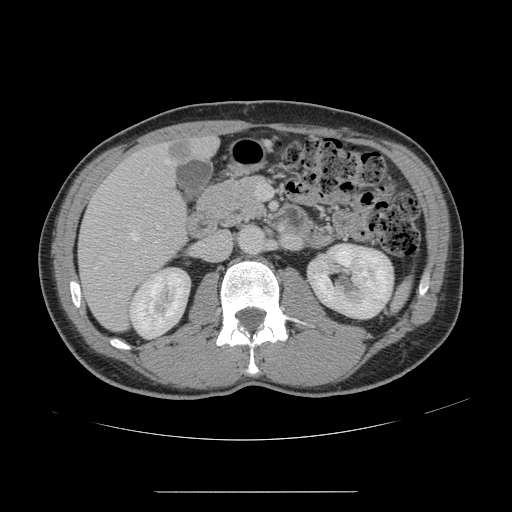
Contrast-enhanced abdominal CT, one axial slice. Slice 67 of 178 in the series (ordered by position). 120 kVp. Intravenous contrast given. Soft-tissue window (W 400 / L 40 HU). 2.5 mm slice thickness. 512 × 512 image matrix, field of view 401 × 401 mm. Male patient, age 53 years. From the clinical record (not read from this slice): diagnosis: colorectal cancer liver metastases, imaged before liver resection; multiple liver metastases: yes; largest metastasis: 2.4 cm.
Structures marked on this image (expert manual segmentation):
- hepatic veins: box from (x=95, y=160) to (x=170, y=270) px
- liver: (x=80, y=138)–(x=216, y=330)
- planned liver remnant (the part of the liver to remain after resection): (x=197, y=138)–(x=216, y=157)
- portal vein (with intrahepatic branches): (x=137, y=184)–(x=267, y=199)
- liver metastasis: (x=168, y=142)–(x=192, y=163)